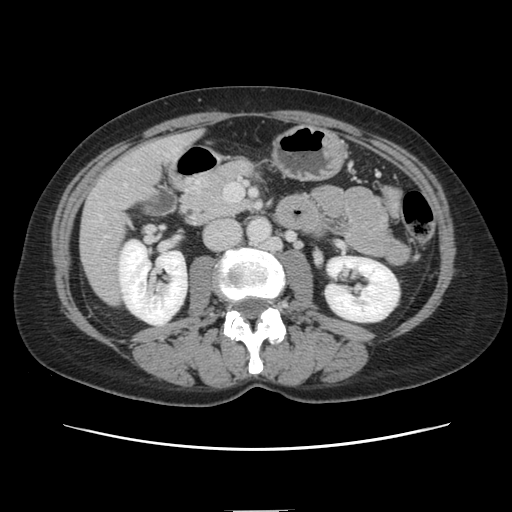
Contrast-enhanced abdominal CT, one axial slice. Position 44 of 141 along the scan axis. 120 kVp. Intravenous contrast given. Soft-tissue window (W 400 / L 40 HU). 2.5 mm slice thickness. 512 × 512 image matrix, field of view 350 × 350 mm. Female patient, age 63 years. Case-level facts recorded for this patient, not image findings: diagnosis: colorectal cancer liver metastases, imaged before liver resection; multiple liver metastases: yes; largest metastasis: 3.2 cm.
Annotated regions visible in this slice (manually delineated by an expert):
- liver: bounding box [x1, y1, x2, y2] px = [81, 133, 198, 305]
- planned liver remnant (the part of the liver to remain after resection): [183, 133, 198, 150]